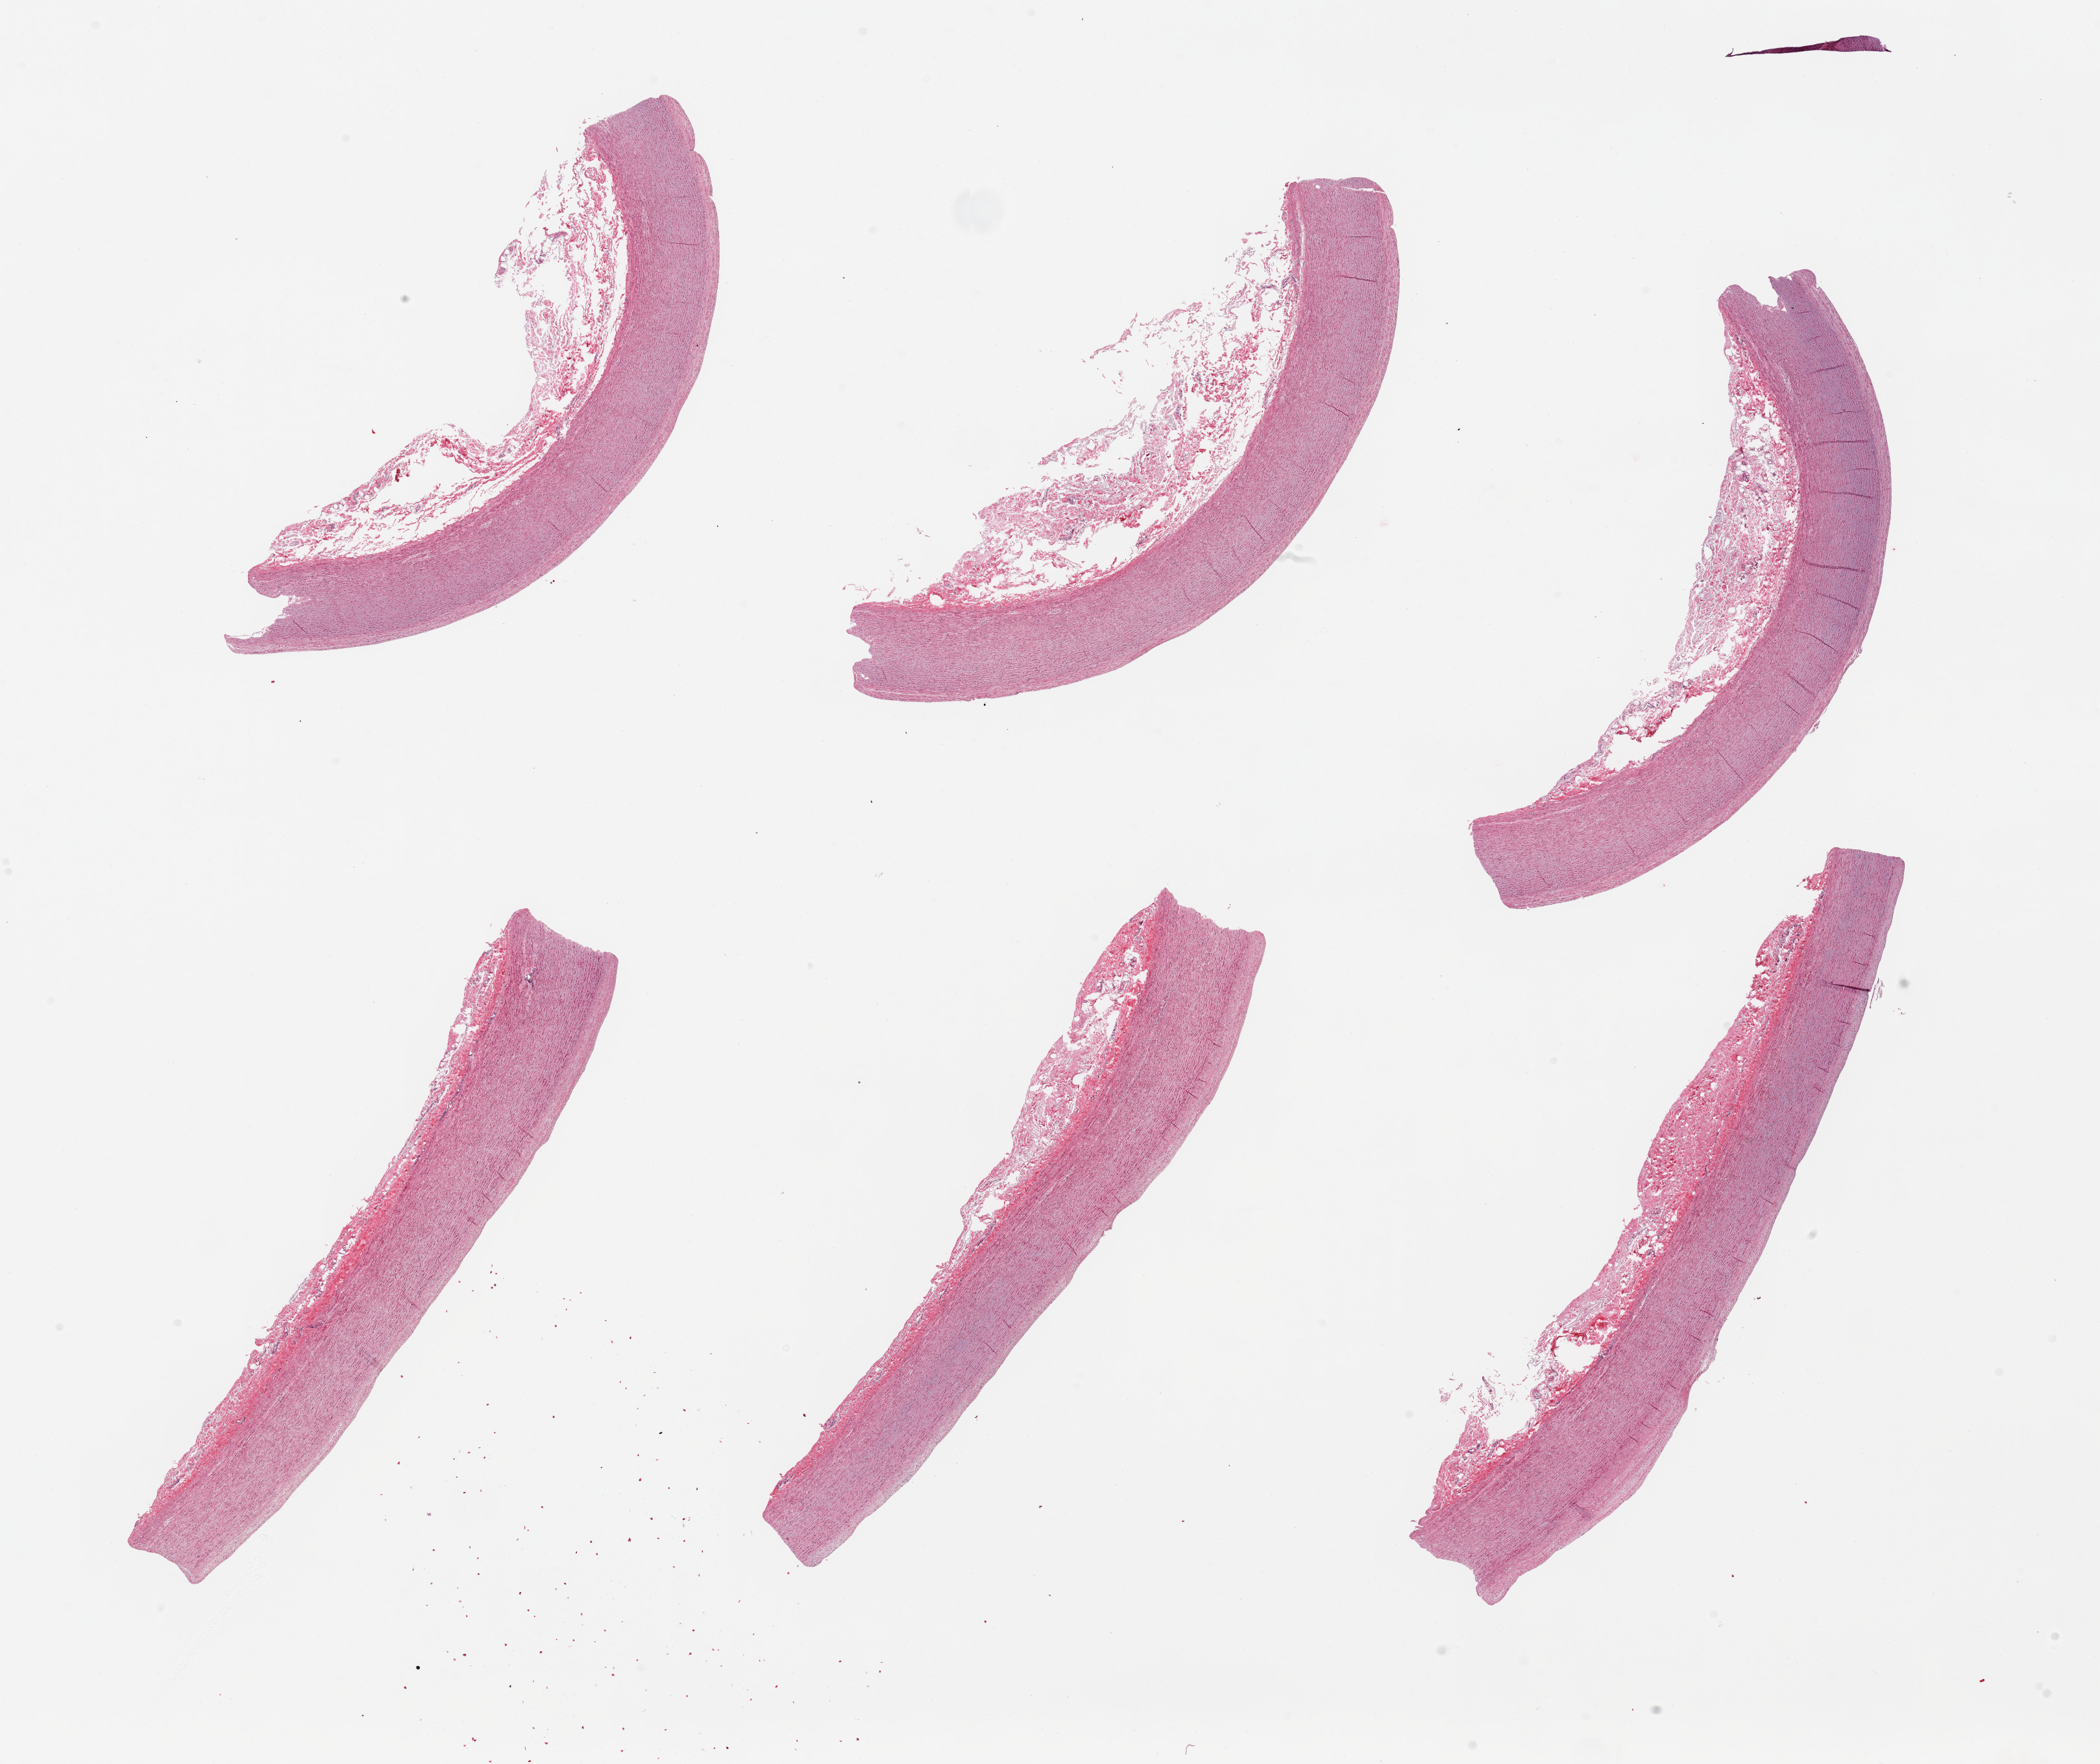
Digitized H&E-stained section, brightfield — low-resolution overview of the scanned area, about 25.6 x 21.5 mm (slide scanned at 20x); PAXgene-fixed paraffin-embedded (PFPE) section; target tissue: aorta; donor tissue sample. Donor: female.
Pathologist's review note for this sample: 6 pieces; no lesions; loose fibrous adventitia, 1mm thick.